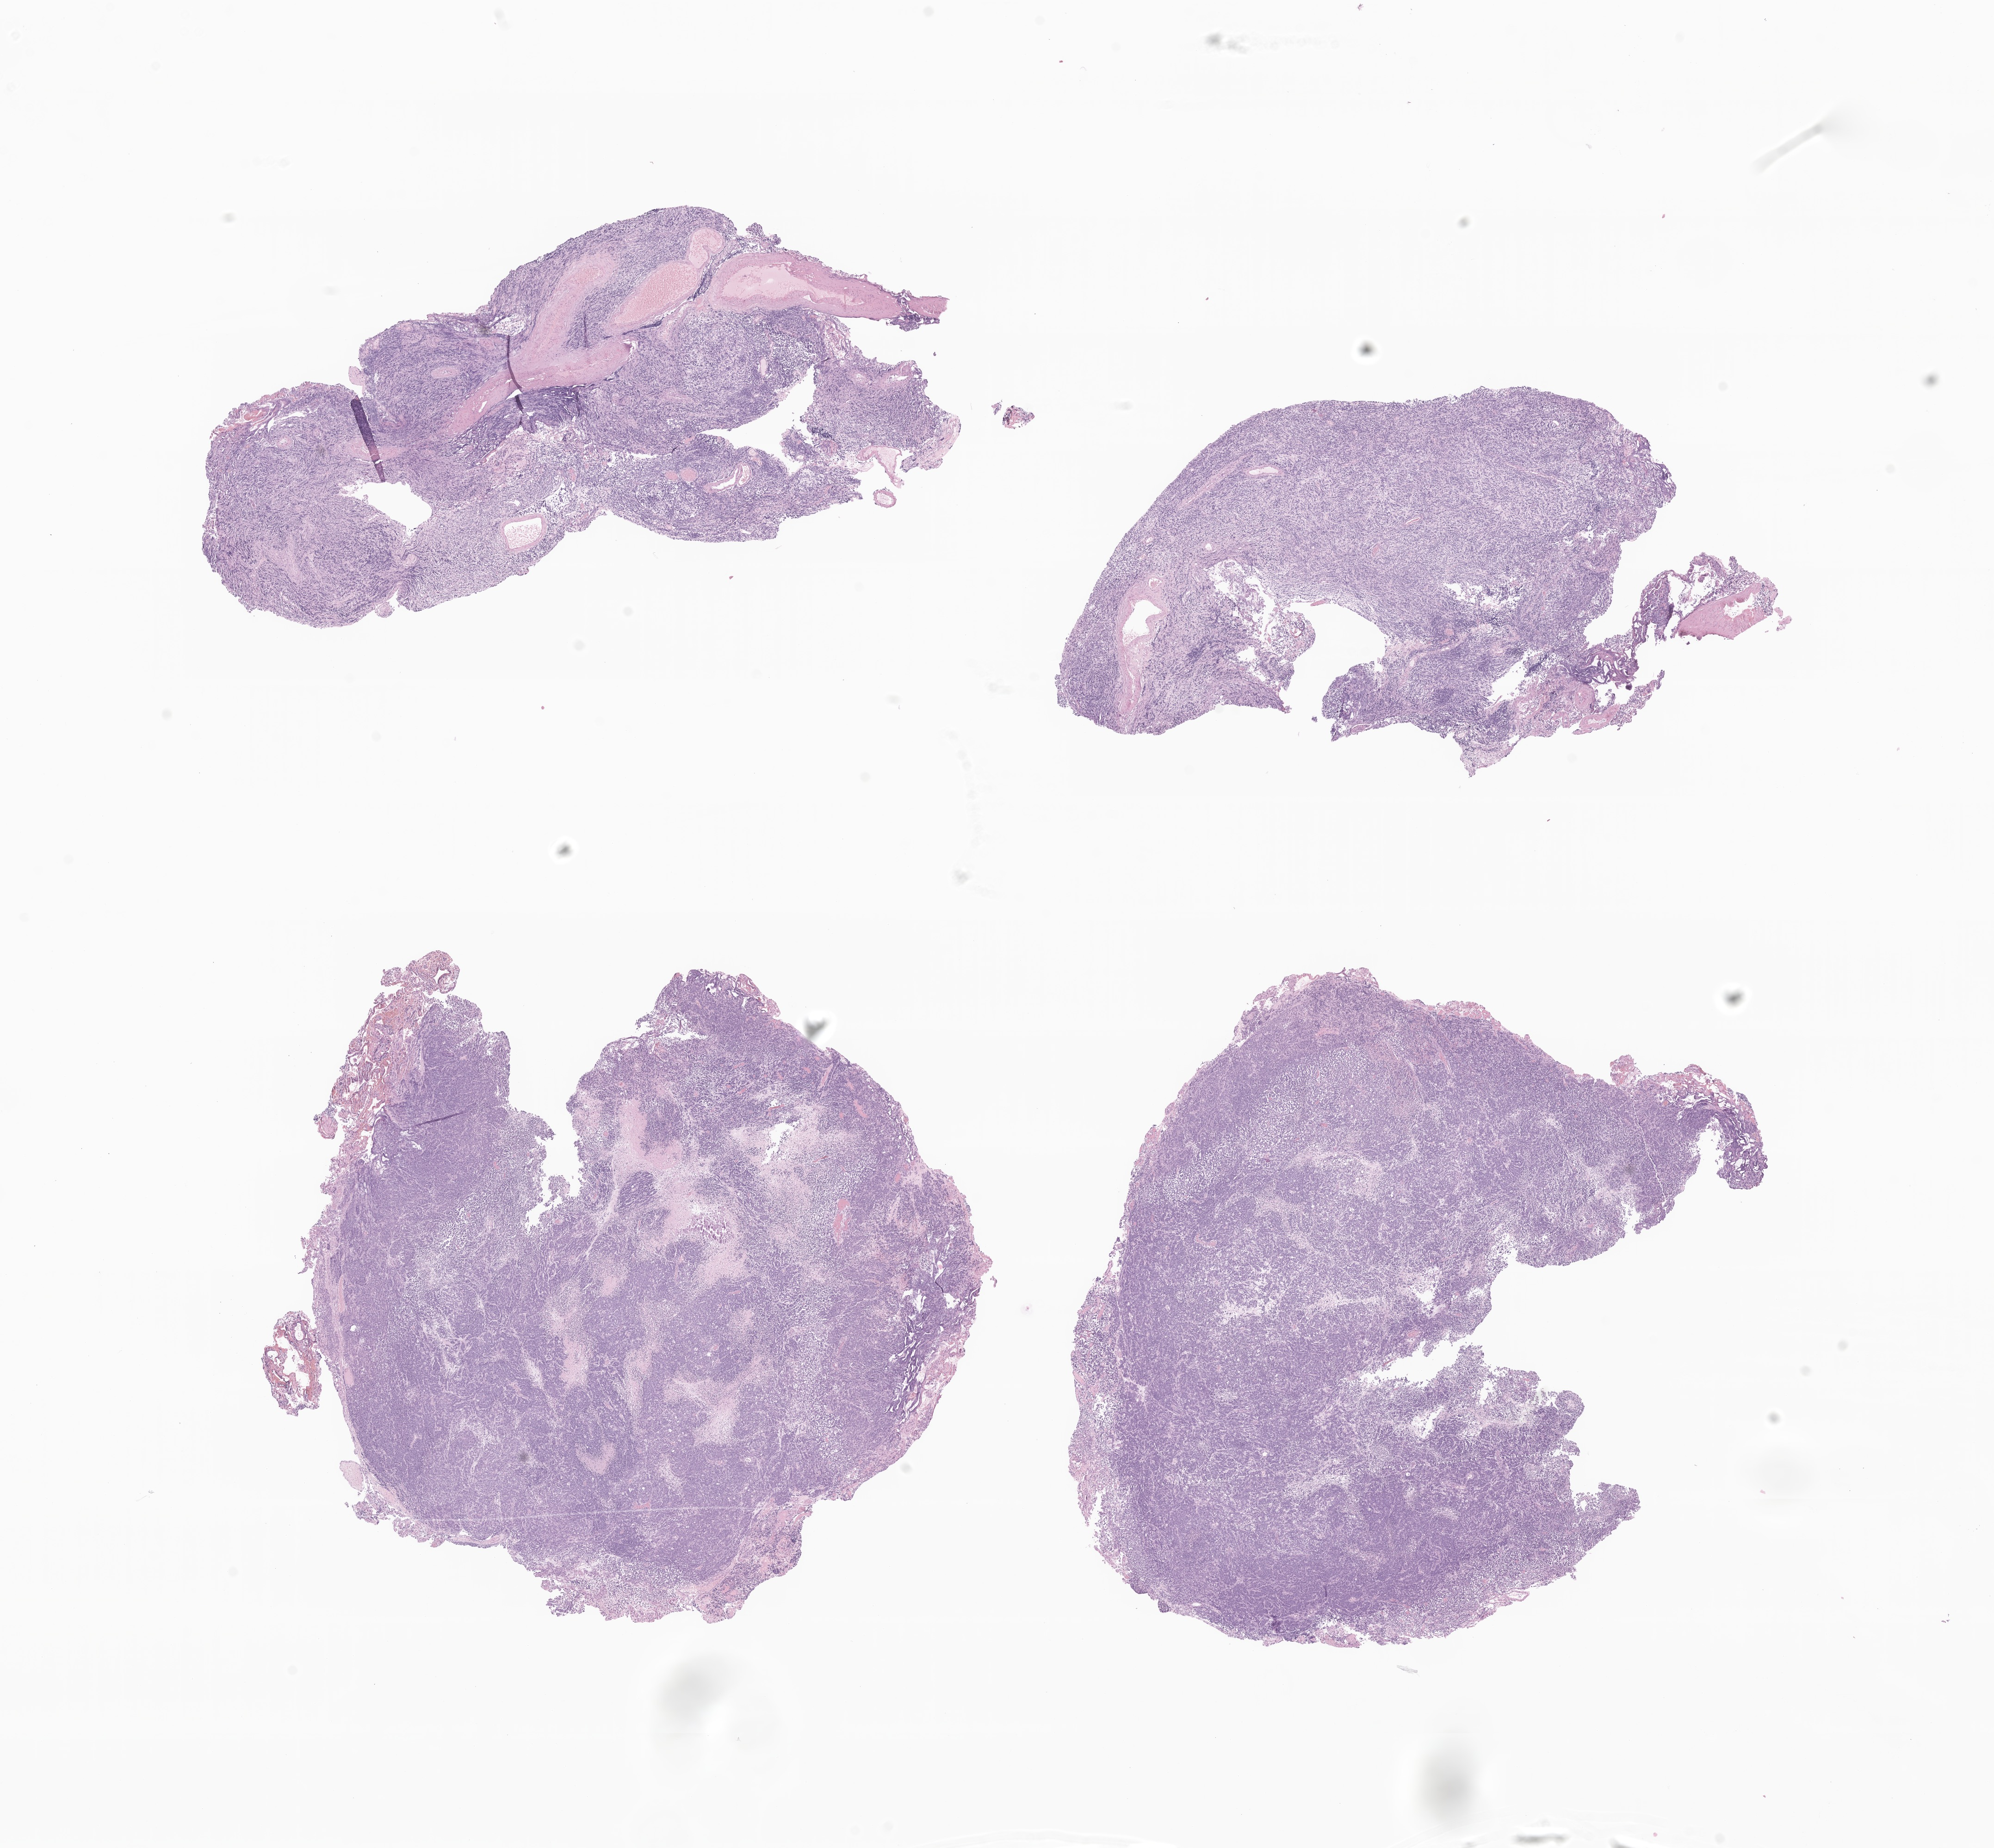
Hematoxylin and eosin (H&E) whole-slide image of tumor tissue from the brain — low-resolution overview of the scanned area, about 18.2 x 16.8 mm, FFPE section. Male patient, age 92 months.
Diagnosis: Neoplasm, malignant.